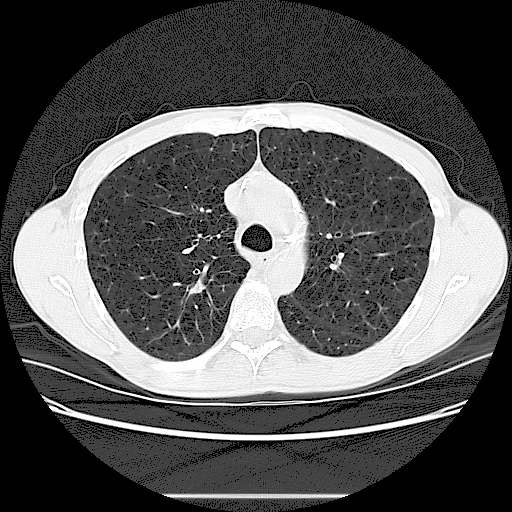
Chest CT (low-dose screening protocol), one axial image, second screening round (one year after baseline), lung window (W 1500 / L -600 HU), 2.5 mm slice thickness, lung (sharp) reconstruction kernel (LUNG), 120 kVp, slice 40 of 131 in the series, 512 × 512 image matrix, field of view 360 × 360 mm. Male, age 59 years at enrolment.
Lesion marked by an expert reader, box from (x=175, y=269) to (x=220, y=314) px. The exam's reader record, not a measurement of the box and not confirmed to be the same lesion: non-calcified nodule or mass ≥4 mm, right upper lobe, 7 × 4 mm, smooth margins, soft tissue attenuation, pre-existing on the prior screen: no. Official screen result: positive, other.